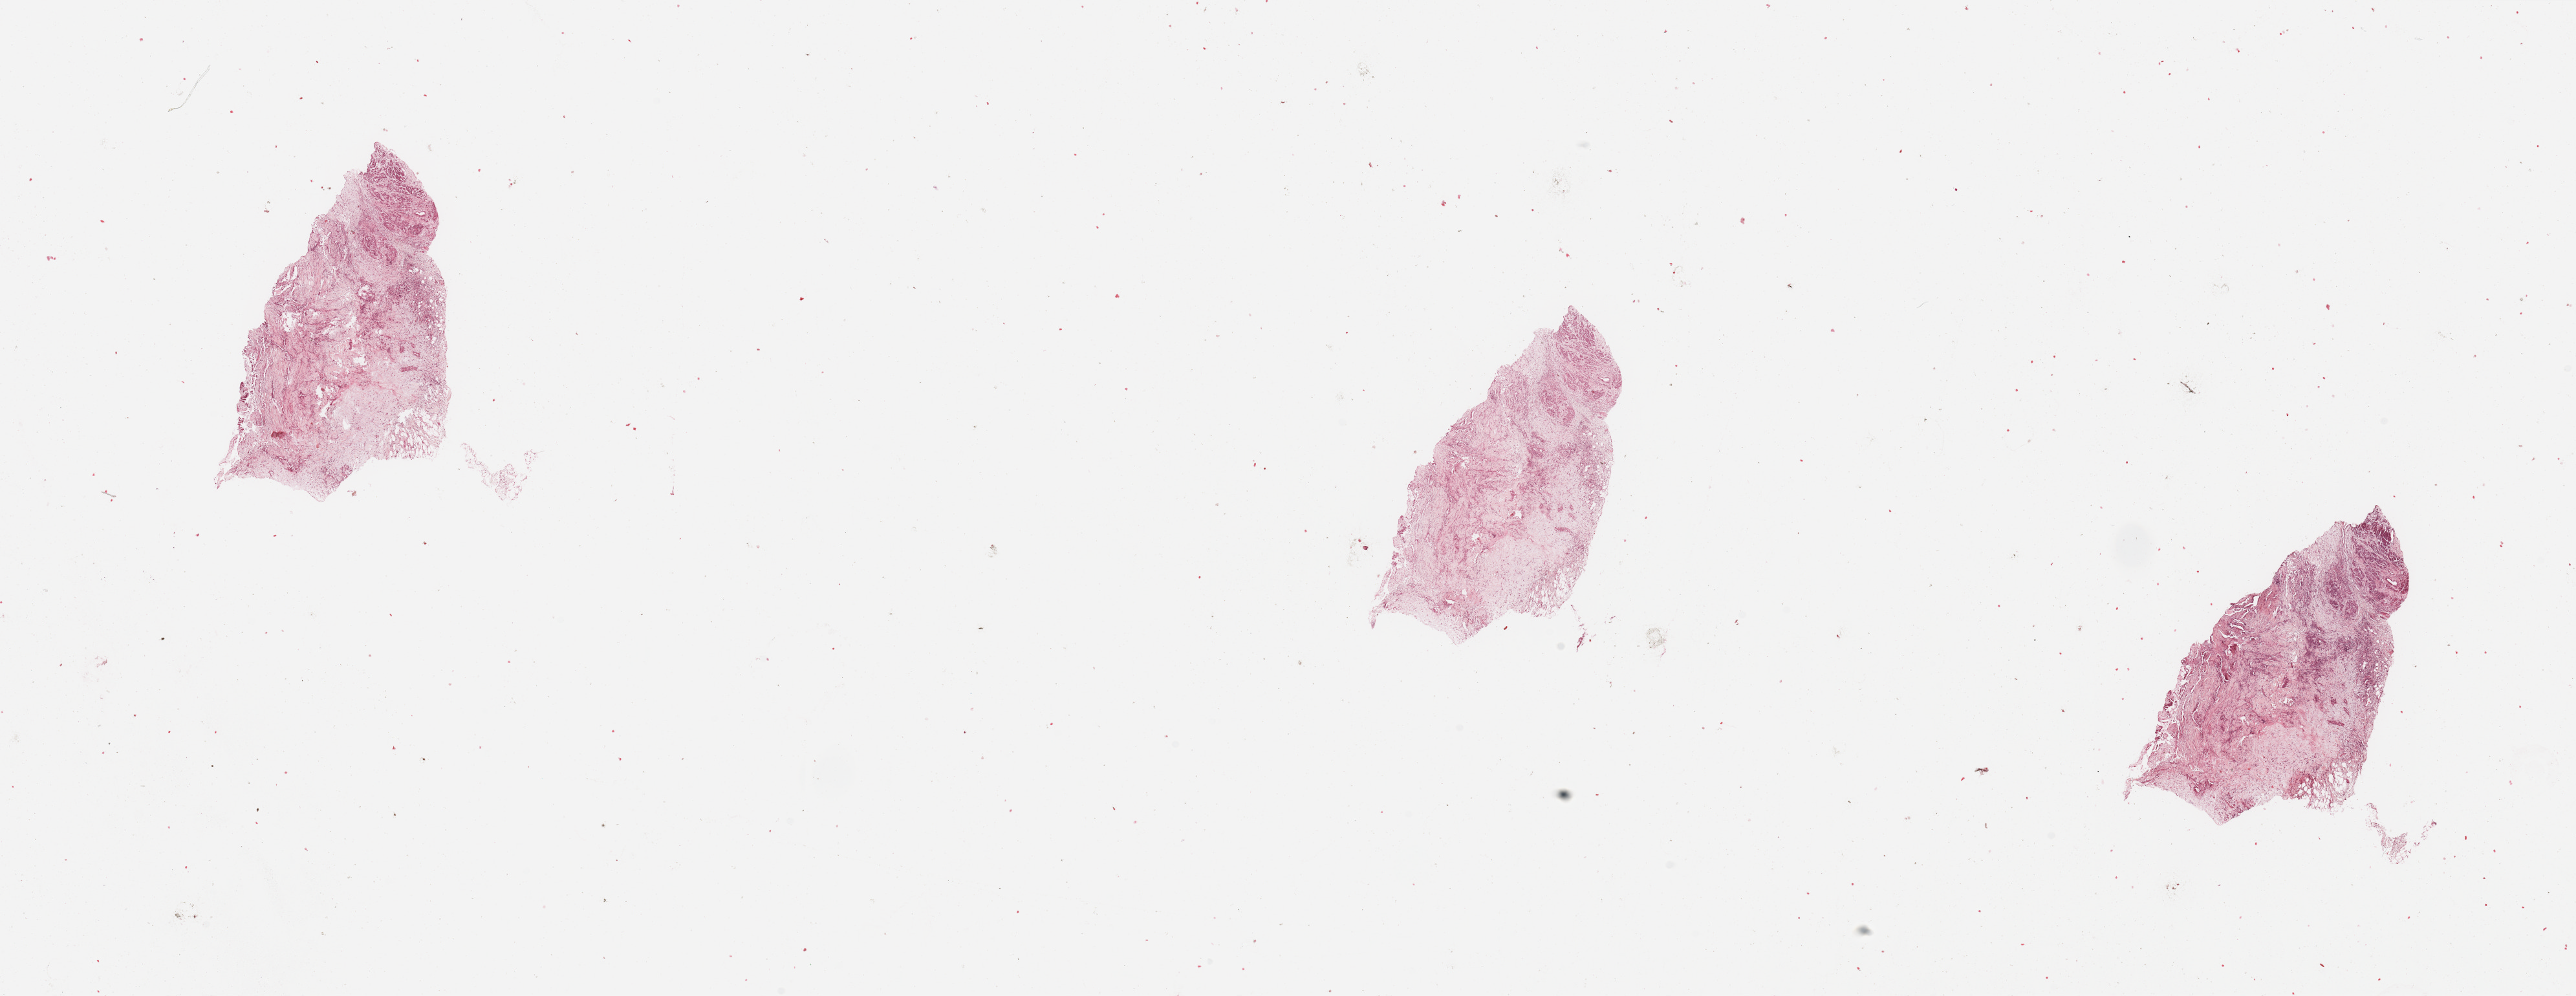
Hematoxylin and eosin (H&E) stained whole-slide image — low-resolution overview of the scanned area, about 31.5 x 12.2 mm (slide scanned at 20x); pancreas, normal (non-tumour) tissue. 63-year-old male patient.
This section: normal (non-tumour) tissue from the same patient. Patient diagnosis: Infiltrating duct carcinoma, NOS.